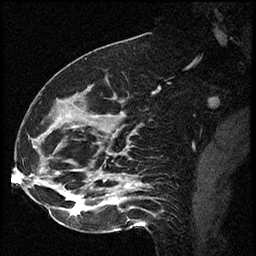
Breast MRI (dynamic contrast-enhanced), one sagittal slice; slice 25 of 60 in the series (ordered by position); dynamic contrast-enhanced series, image 2 of 2 at this slice position (ordered by acquisition); 1.5 T; TE 4.2 ms, TR 17.3 ms; 2 mm slice thickness; 256 × 256 image matrix, field of view 200 × 200 mm. Female patient. Case-level facts recorded for this patient, not image findings: setting: breast cancer imaged before/during neoadjuvant chemotherapy; receptor status: HR-positive, HER2-negative.
Structures marked on this image (semi-automatic segmentation, software-assisted and operator-edited):
- analysis volume of interest (the breast-tissue region the enhancement analysis was run in; not a lesion): bounding box (x1, y1, x2, y2) in pixels: (41, 93, 115, 223)
- tumour enhancement mask (voxels above the 100 % enhancement threshold inside the analysis volume of interest): (69, 195, 84, 214)